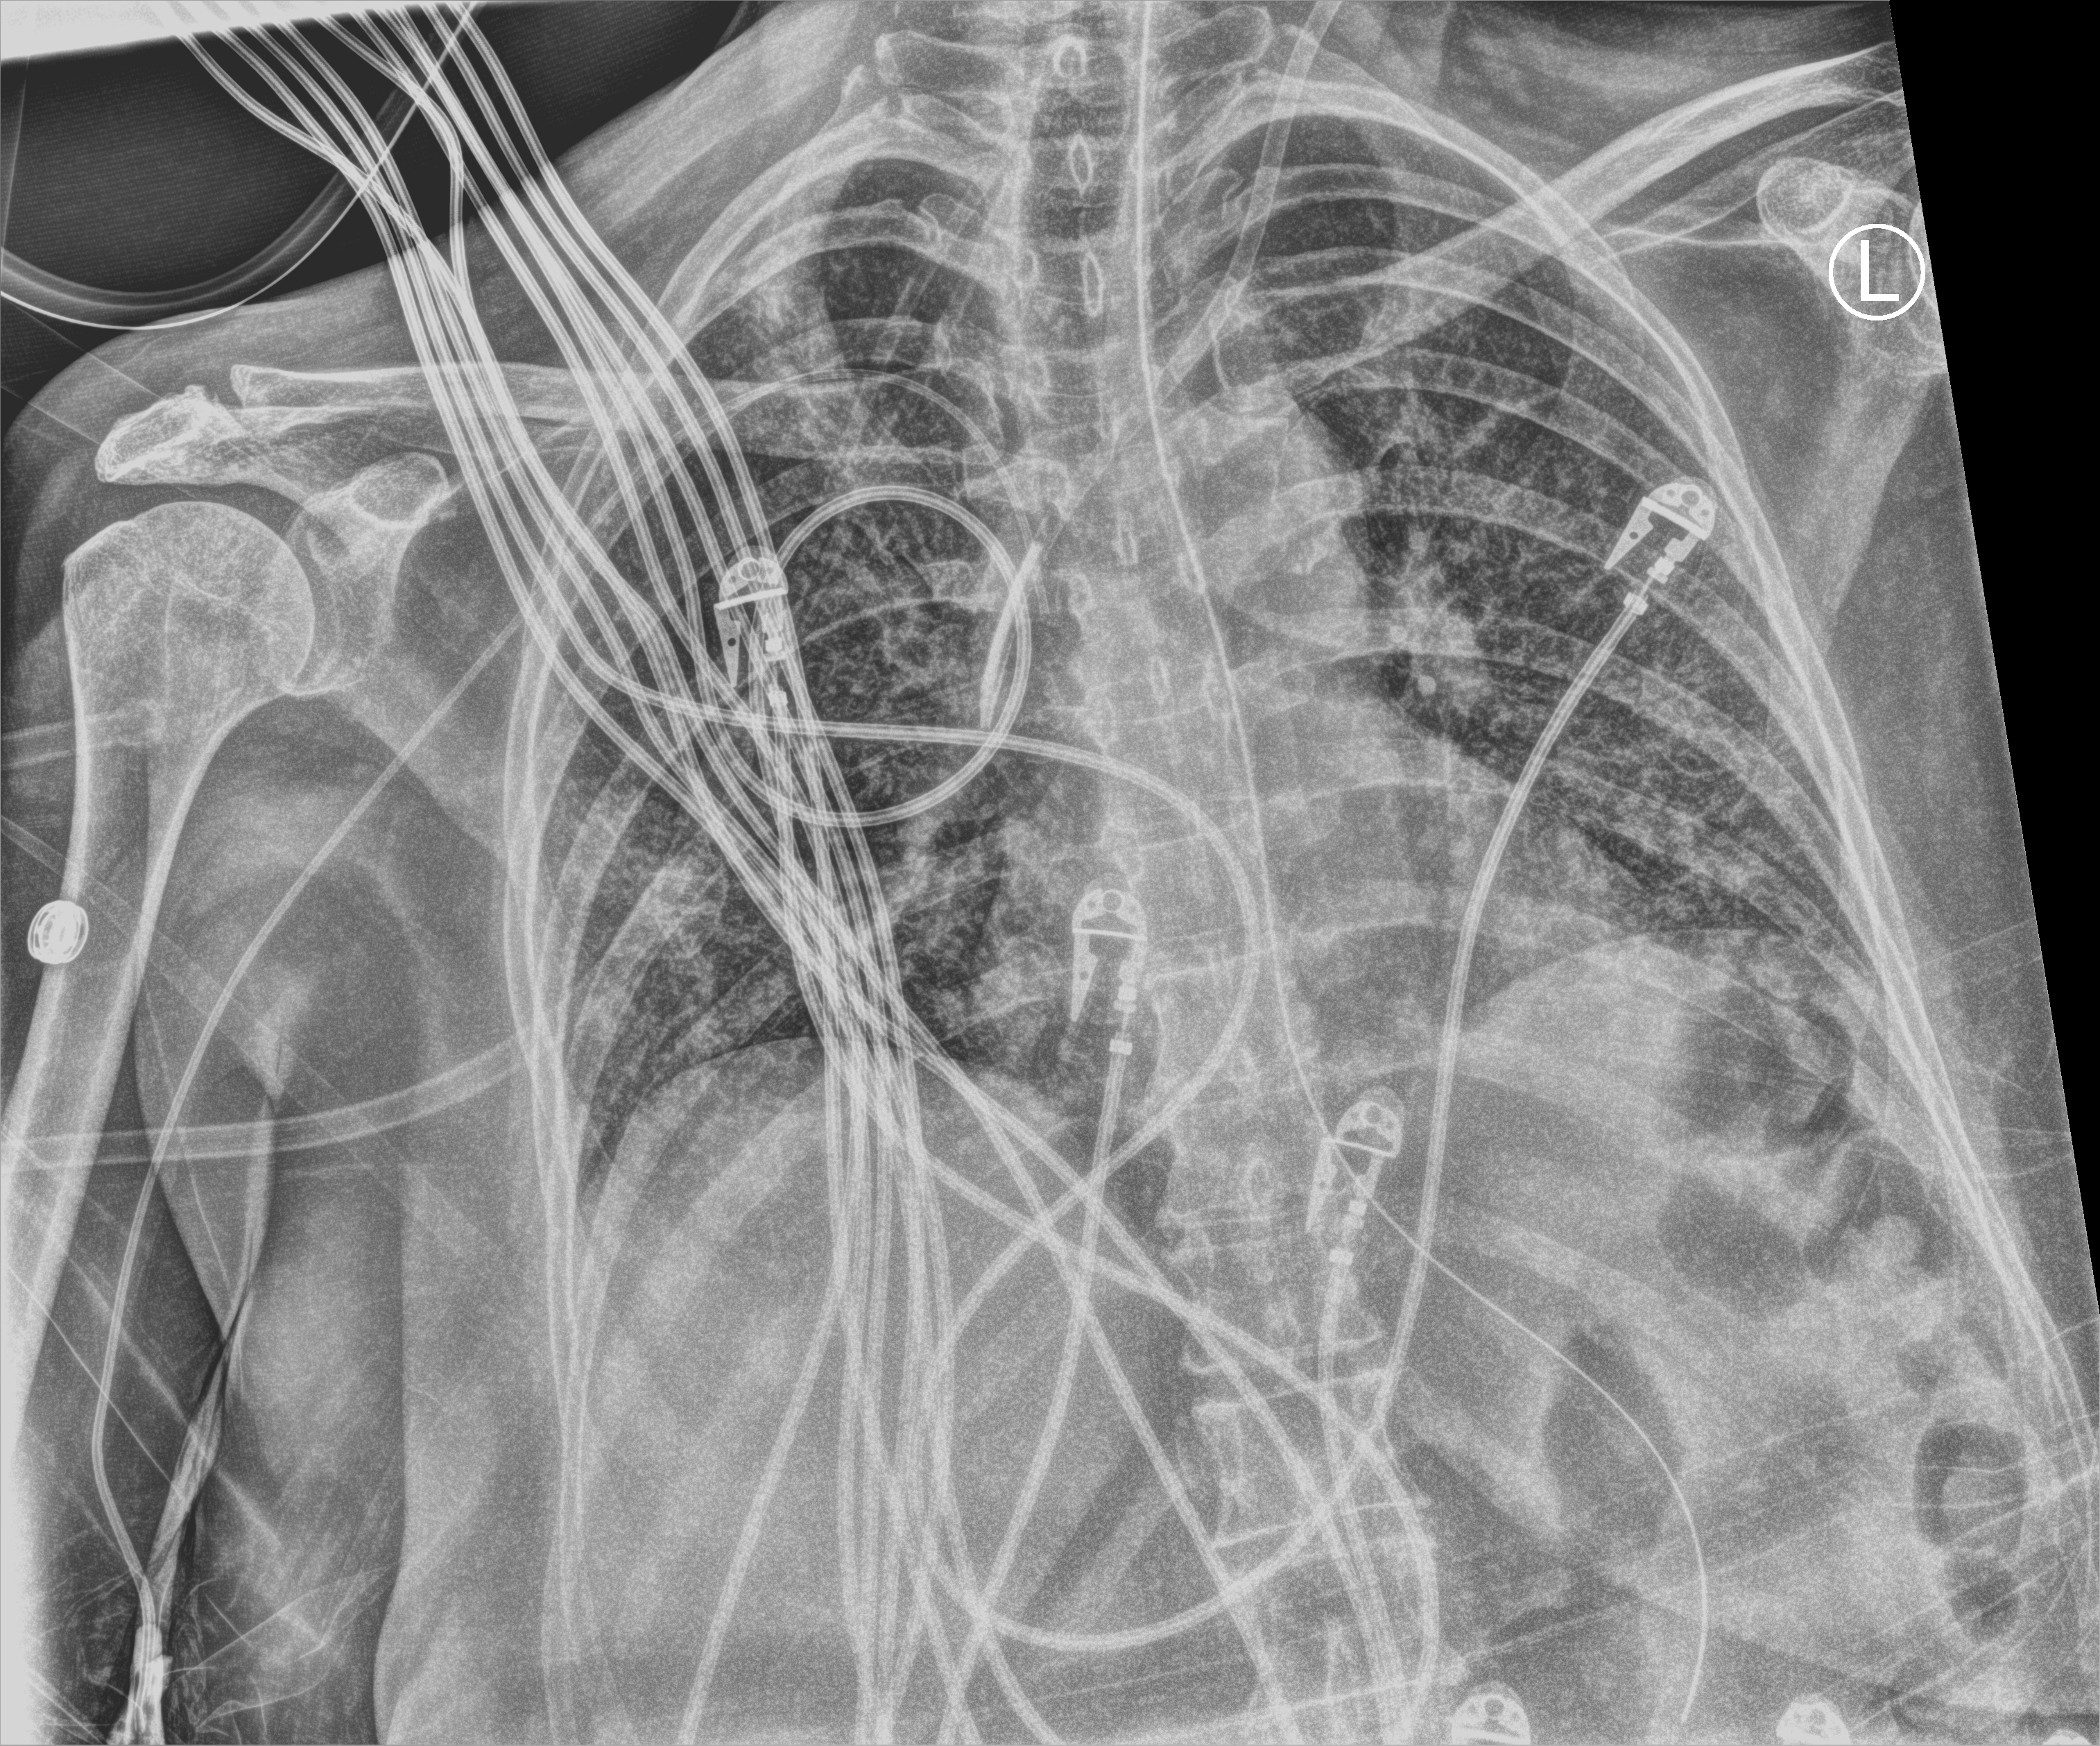
Chest X-ray (portable); anteroposterior (AP) projection. Female patient hospitalised with COVID-19, age 60–74 years.
From the hospital-stay record, not from the radiograph (when in the stay this image was taken is not recorded): length of hospital stay: 43 days.